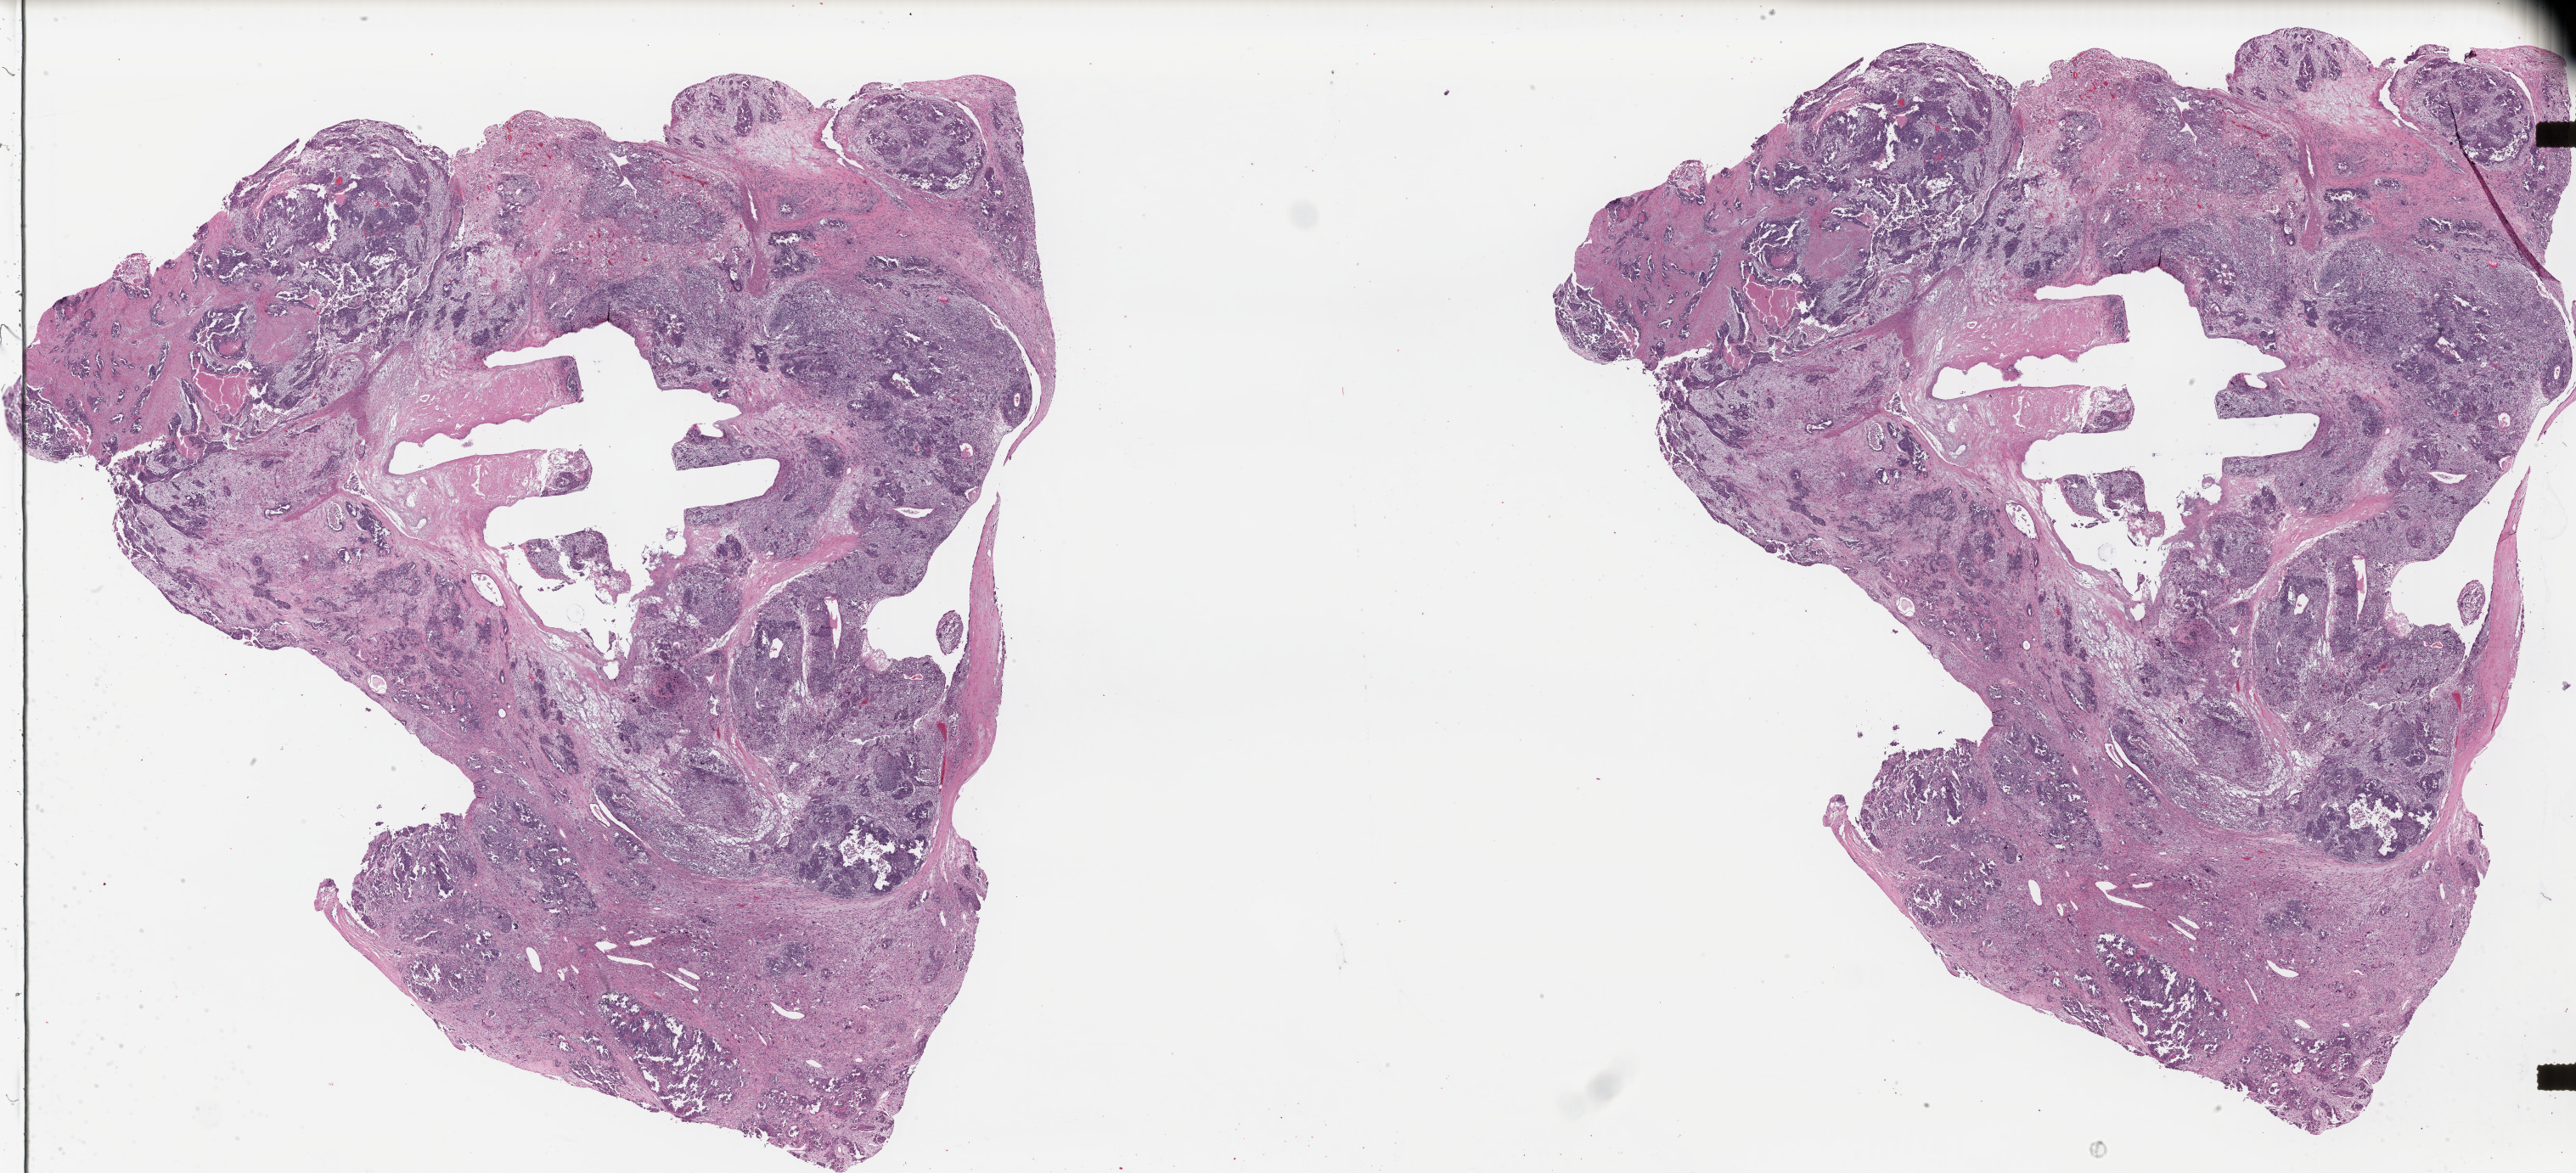
Whole-slide histology image, H&E — whole scanned area (about 47.7 x 21.7 mm, from a 40x scan) shown as a low-resolution overview. FFPE section. Primary tumour sample from the uterus. Female patient; age at initial diagnosis 75 years.
* FIGO stage: IB
* pathologic diagnosis: Mullerian mixed tumor (endometrium)